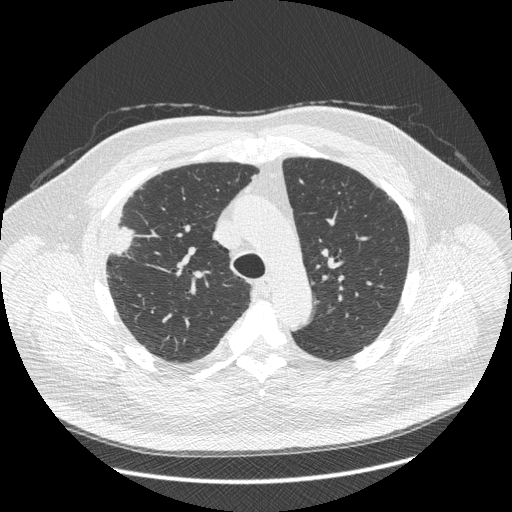
Axial slice from a low-dose chest CT screening exam, third annual screen, lung window (W 1500 / L -600 HU), standard (soft-tissue) reconstruction kernel (STANDARD), slice 119 of 426 in the series. Male participant, aged 66 years at enrolment. Current smoker at enrolment.
Lesion marked by an expert reader, box from (x=87, y=206) to (x=147, y=270) px. Reader record for this screening exam (exam-level; its link to the box is not recorded): non-calcified nodule or mass ≥4 mm, right upper lobe, 48 × 25 mm, spiculated (stellate) margins, soft tissue attenuation, pre-existing on the prior screen: no. Official screen result: positive, other. Lung cancer was diagnosed 35 days after this screen: non-small cell carcinoma, right upper lobe, stage IV (AJCC 6th edition), 50 mm at pathology.